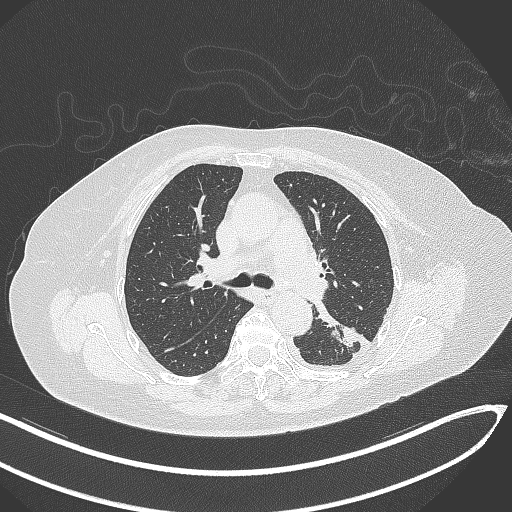
Chest CT, one axial slice; position 203 of 270 along the scan axis; 120 kVp; lung window (W 1500 / L -600 HU); 1 mm slice thickness; 512 × 512 image matrix, field of view 400 × 400 mm. Patient: female, 76 years. From the clinical record (not read from this slice): clinical TNM (as recorded): T1c N0 M0.
Annotated regions visible in this slice (rectangle marked by the reading radiologist):
- lung tumour (recorded histology: adenocarcinoma): bounding box <313,307,362,352> (left, top, right, bottom; pixels)